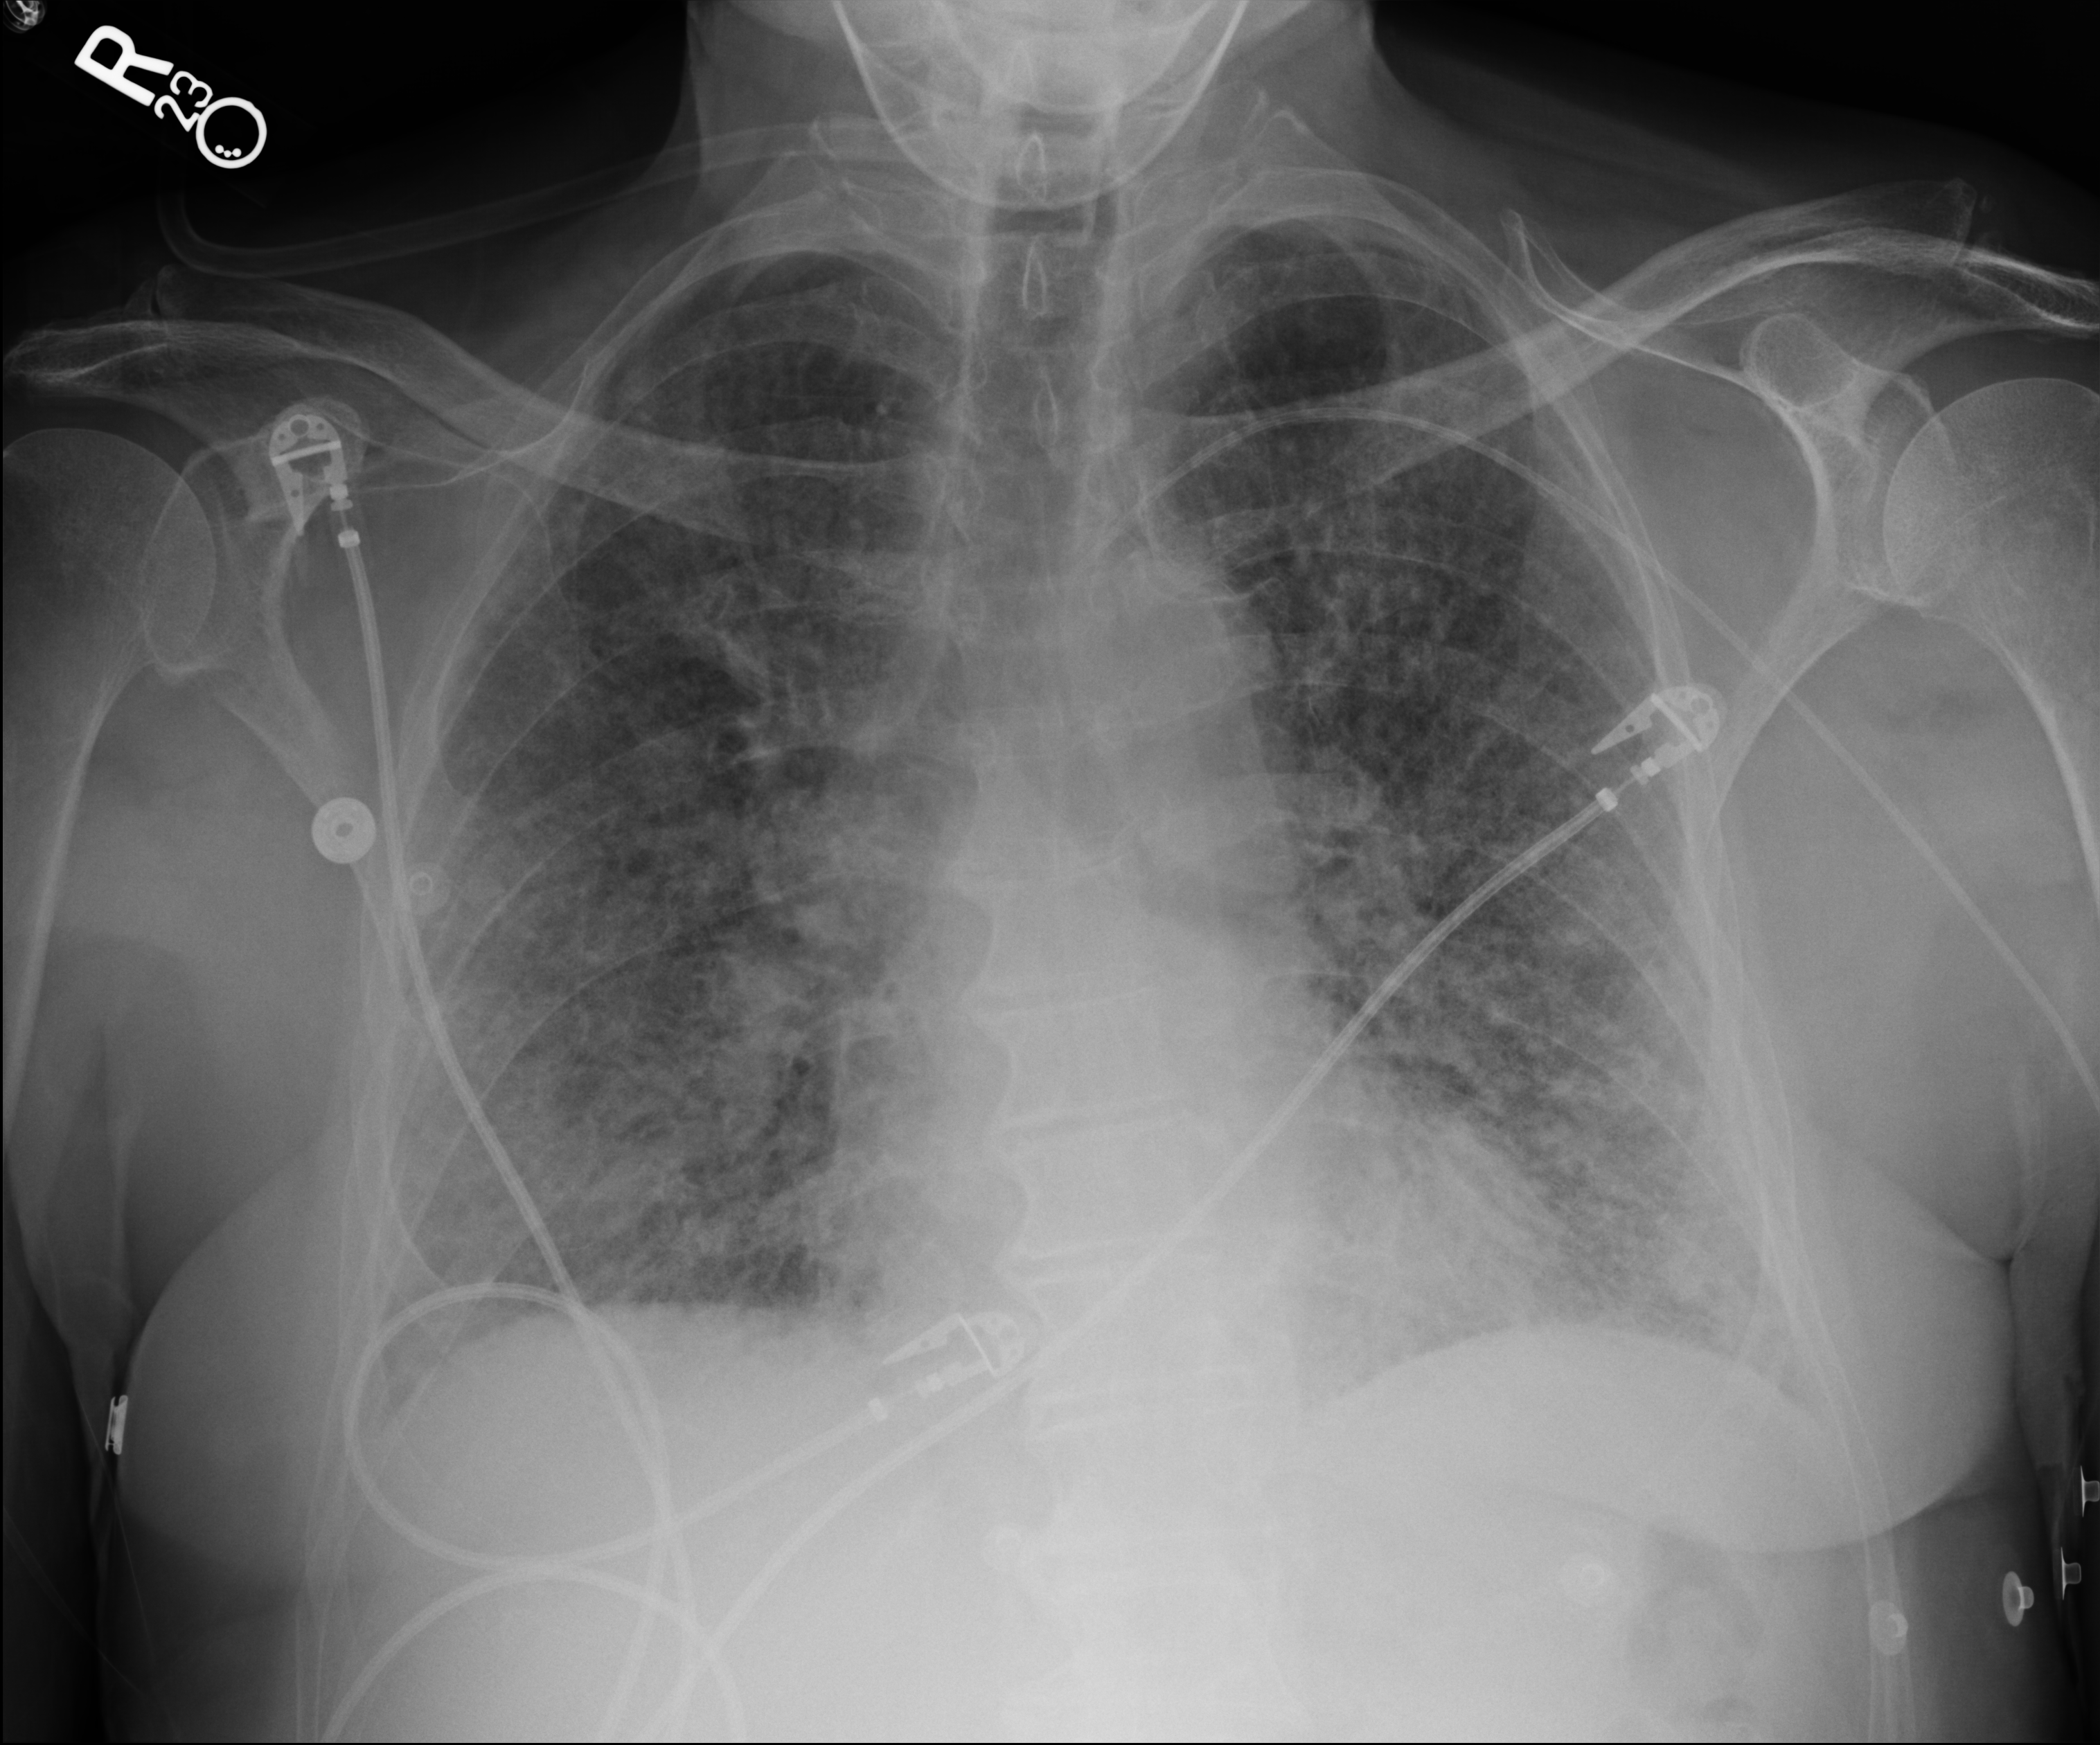
Bedside chest radiograph (computed radiography); anteroposterior (AP) projection. Patient hospitalised with COVID-19; male, aged 75–90 years.
Admission-level facts for this patient (not findings on this image; timing relative to this image not recorded): length of hospital stay: 47 days; mechanically ventilated during this hospital stay: yes.